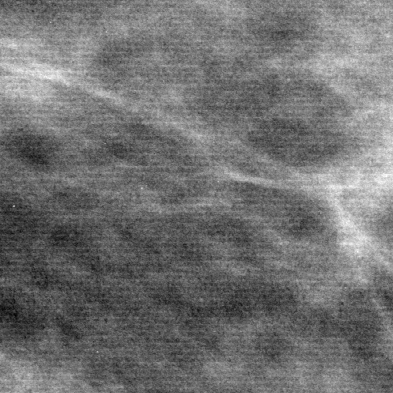
Cropped region of a digitized screen-film mammogram centred on a radiologist-marked abnormality, left breast, MLO view.
Calcifications, morphology pleomorphic, distribution clustered; BI-RADS assessment category 4; subtlety rating 4 on a 1 (subtle) to 5 (obvious) scale; pathology (as recorded): benign.